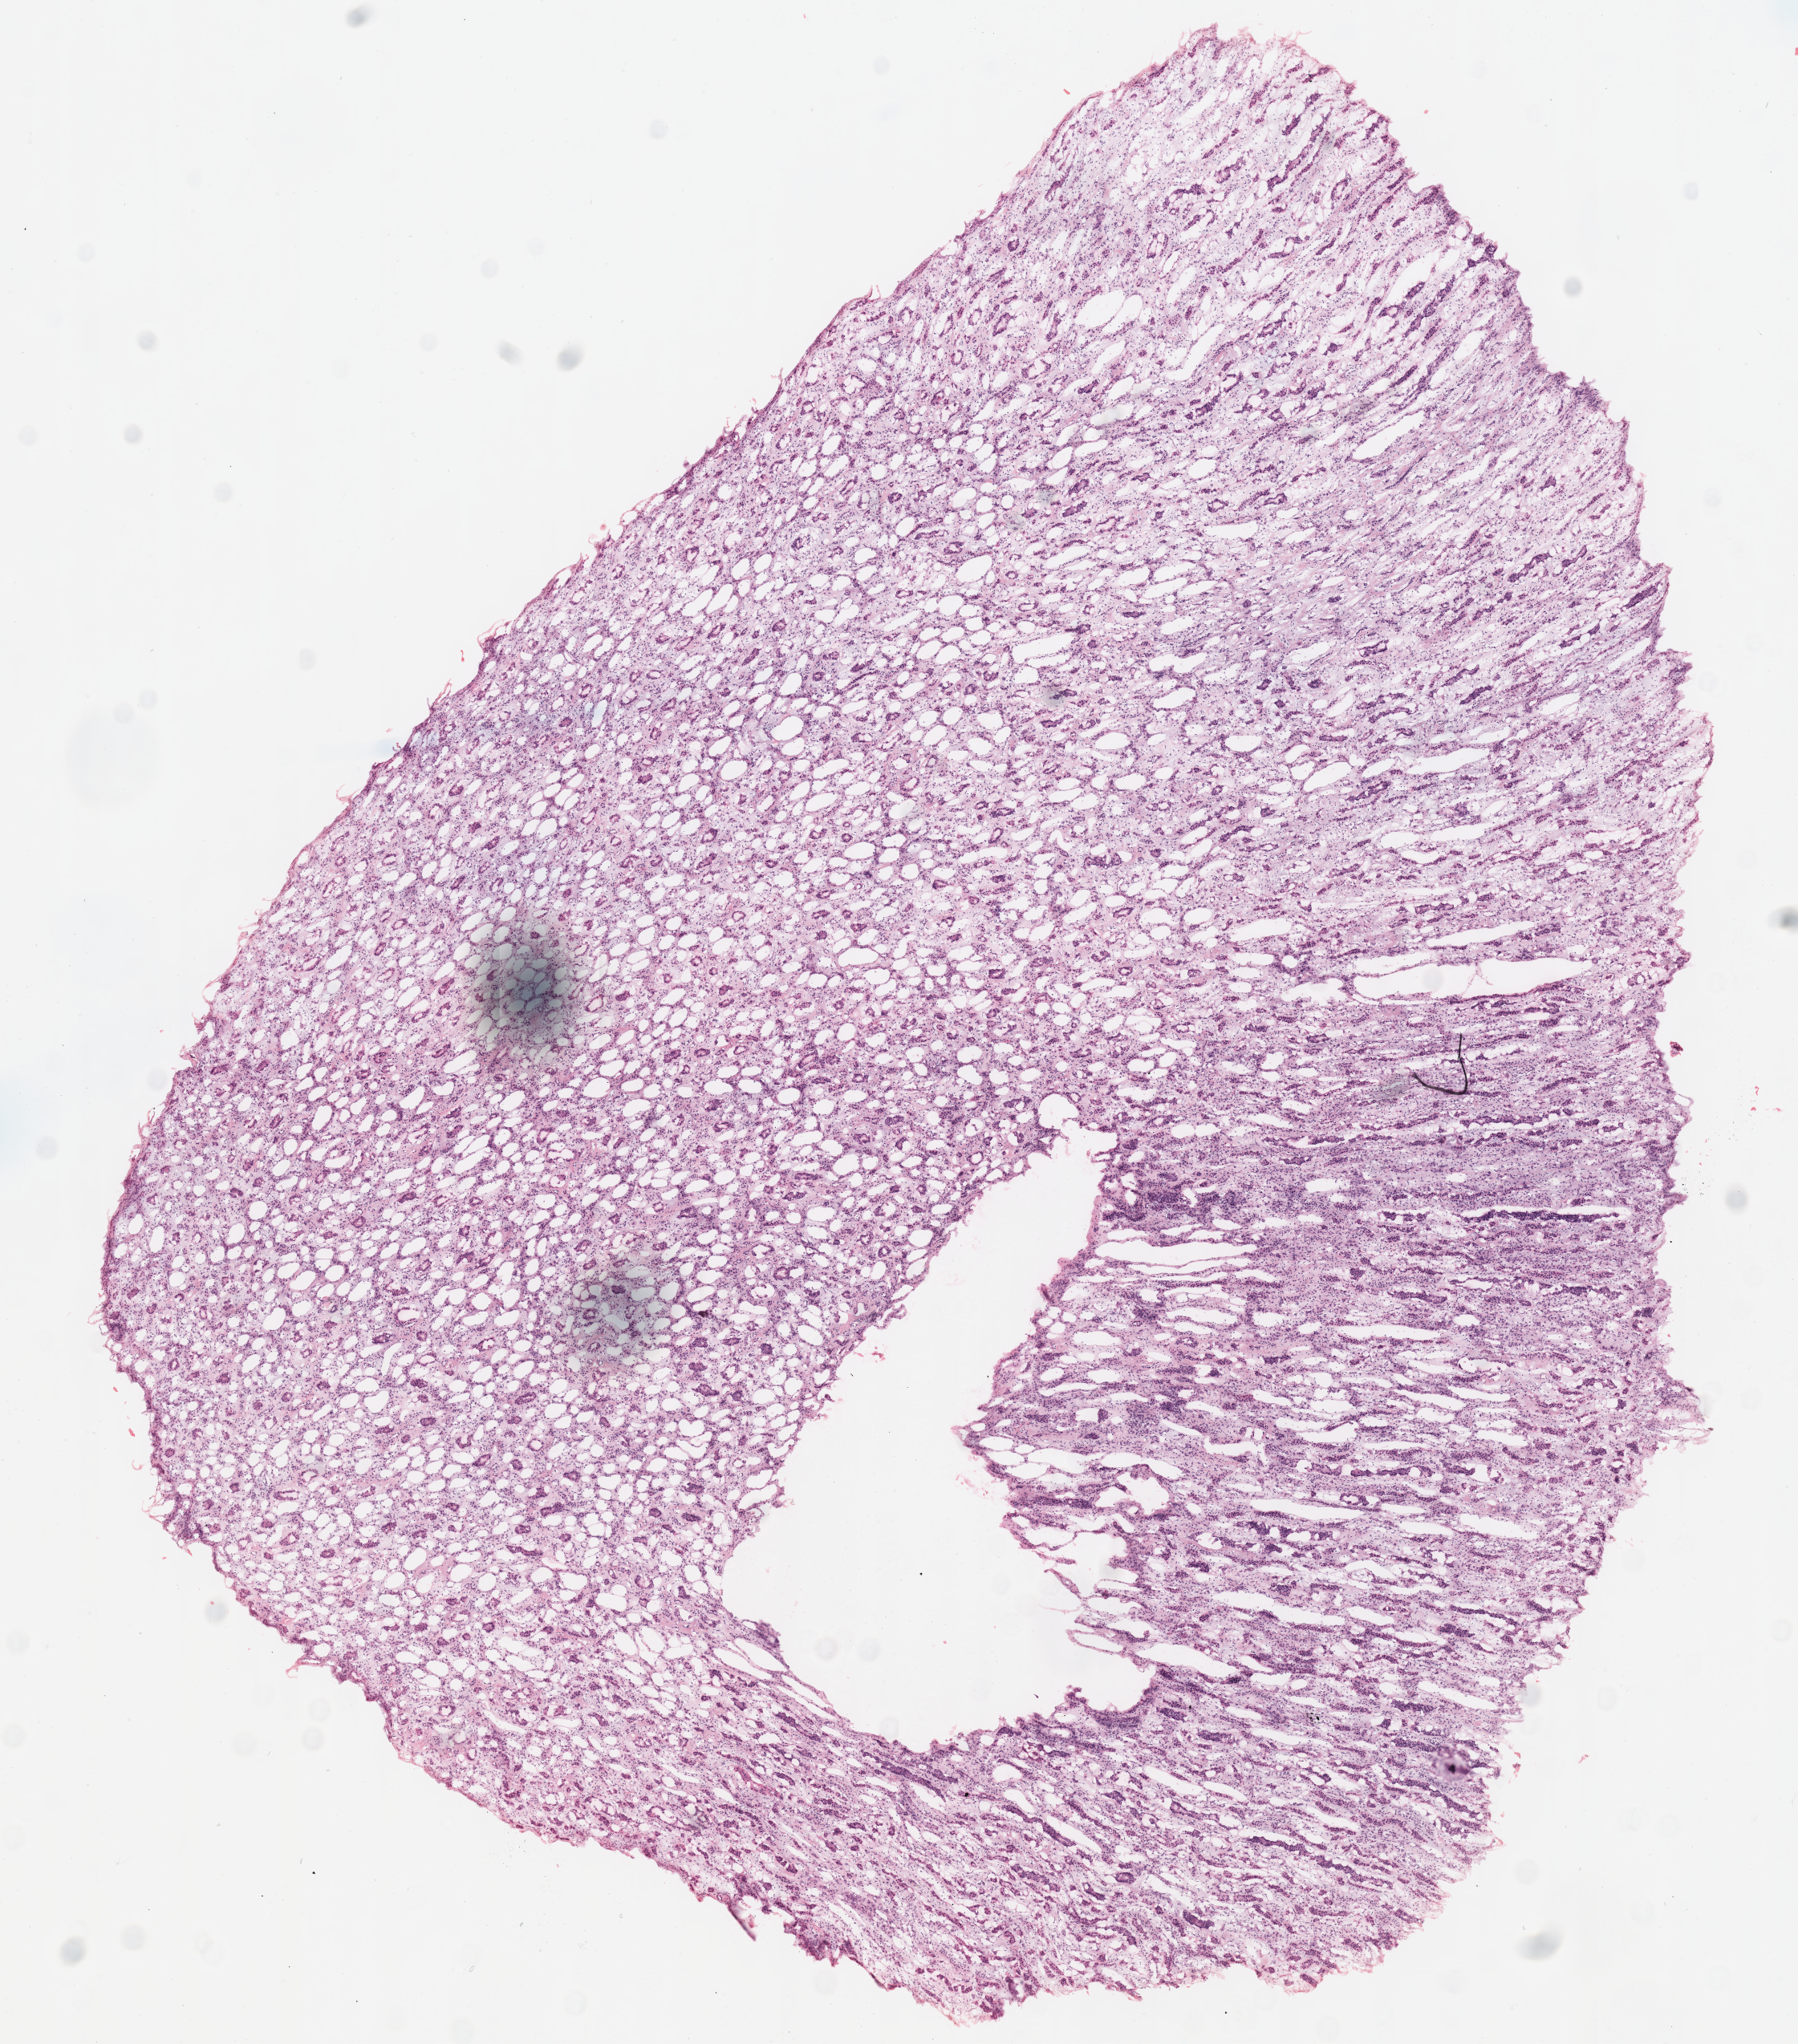
Hematoxylin and eosin (H&E) stained whole-slide image, a low-resolution overview of the entire scanned area, about 8.8 x 10.0 mm (acquisition: 40x scan). Frozen section from the top of the tissue portion. Kidney, solid tissue normal (non-tumour tissue) sample. Male patient; age at initial diagnosis 44 years. Inflammatory infiltration, as recorded: lymphocyte infiltration 0%, monocyte infiltration 0%, neutrophil infiltration 0%.
- this section: solid tissue normal (non-tumour) sample from the same patient
- patient diagnosis: Renal cell carcinoma, chromophobe type